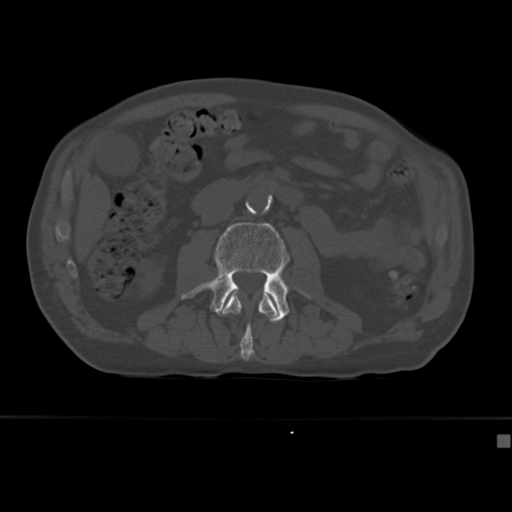
CT including the spine, one axial slice; position 135 of 430 along the scan axis; 120 kVp; bone window (W 1800 / L 400 HU); 1.5 mm slice thickness; 512 × 512 image matrix, field of view 337 × 337 mm. Patient: male, 64 years. From the clinical record (not read from this slice): primary cancer: uterus; vertebrae with lytic lesions (as recorded): T1, T4, T5, T7, L5.
Structures marked on this image (semi-automatic segmentation, software-assisted and operator-edited):
- L2 vertebra: bounding box (x1, y1, x2, y2) in pixels: (220, 292, 279, 361)
- L3 vertebra: (181, 222, 305, 323)